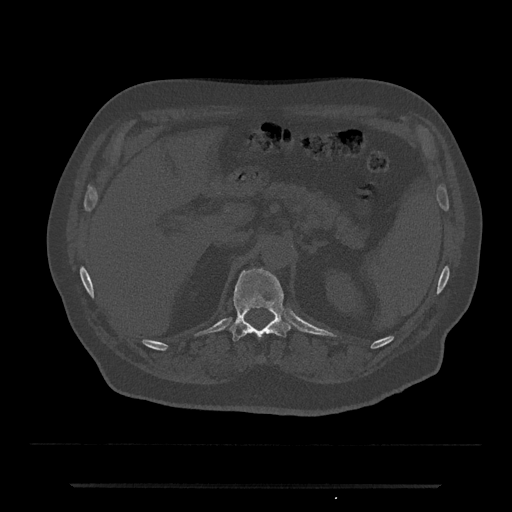
CT including the spine, one axial slice; position 596 of 797 along the scan axis; 120 kVp; bone window (W 1800 / L 400 HU); 512 × 512 image matrix, field of view 434 × 434 mm. Patient: male, 80 years. From the clinical record (not read from this slice): primary cancer: prostate.
Outlined on this slice (semi-automatic segmentation, software-assisted and operator-edited):
- T12 vertebra: bounding box [x1, y1, x2, y2] px = [229, 267, 291, 341]